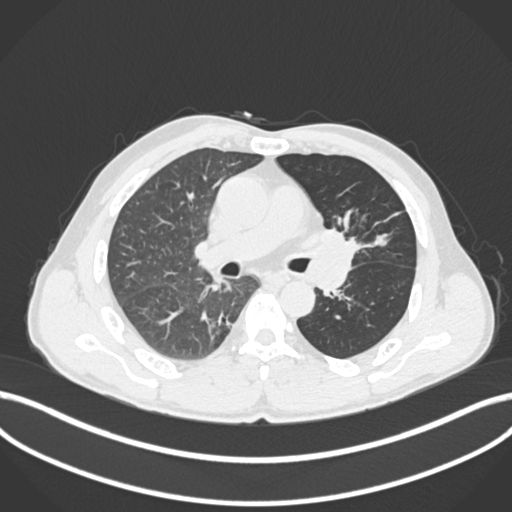
Chest CT, one axial slice; slice 109 of 255 in the series (ordered by position); reconstruction kernel B30f; 120 kVp; lung window (W 1500 / L -600 HU); 1 mm slice thickness; 512 × 512 image matrix, field of view 400 × 400 mm. Male patient, age 57 years. From the clinical record (not read from this slice): clinical TNM (as recorded): T2b N0 M0.
Outlined on this slice (bounding box drawn by a radiologist):
- lung tumour (recorded histology: squamous cell carcinoma): bounding box <308,221,364,264> (left, top, right, bottom; pixels)